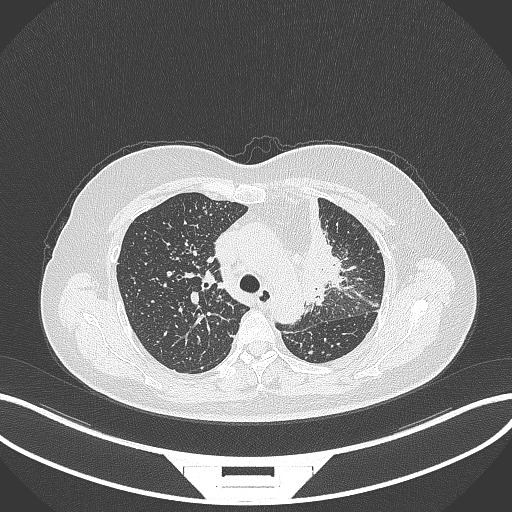
Chest CT, one axial slice. Position 235 of 348 along the scan axis. Reconstruction kernel B70f. Lung window (W 1500 / L -600 HU). 512 × 512 image matrix, field of view 400 × 400 mm. Female patient, age 49 years. Case-level facts recorded for this patient, not image findings: clinical TNM (as recorded): T1c N0 M1.
Structures marked on this image (rectangle marked by the reading radiologist):
- lung tumour (recorded histology: adenocarcinoma): bounding box (x1, y1, x2, y2) in pixels: (289, 193, 348, 308)